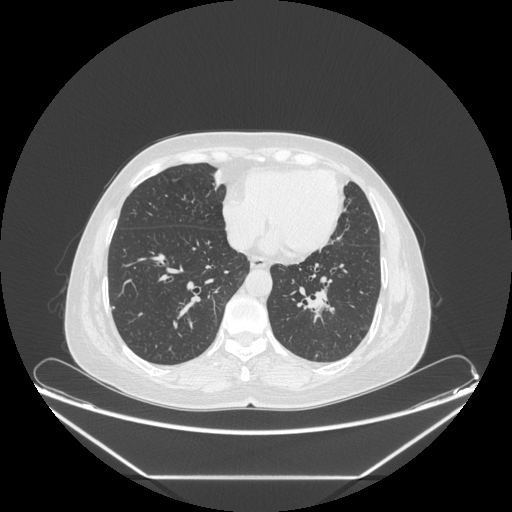
Chest CT, one axial slice. Reconstruction kernel STANDARD. Lung window (W 1500 / L -600 HU). 512 × 512 image matrix. Patient: female, 63 years. Case-level facts recorded for this patient, not image findings: clinical TNM (as recorded): T1c N0 M0.
Outlined on this slice (bounding box drawn by a radiologist):
- lung tumour (recorded histology: adenocarcinoma): bounding box [x1, y1, x2, y2] px = [296, 280, 332, 323]